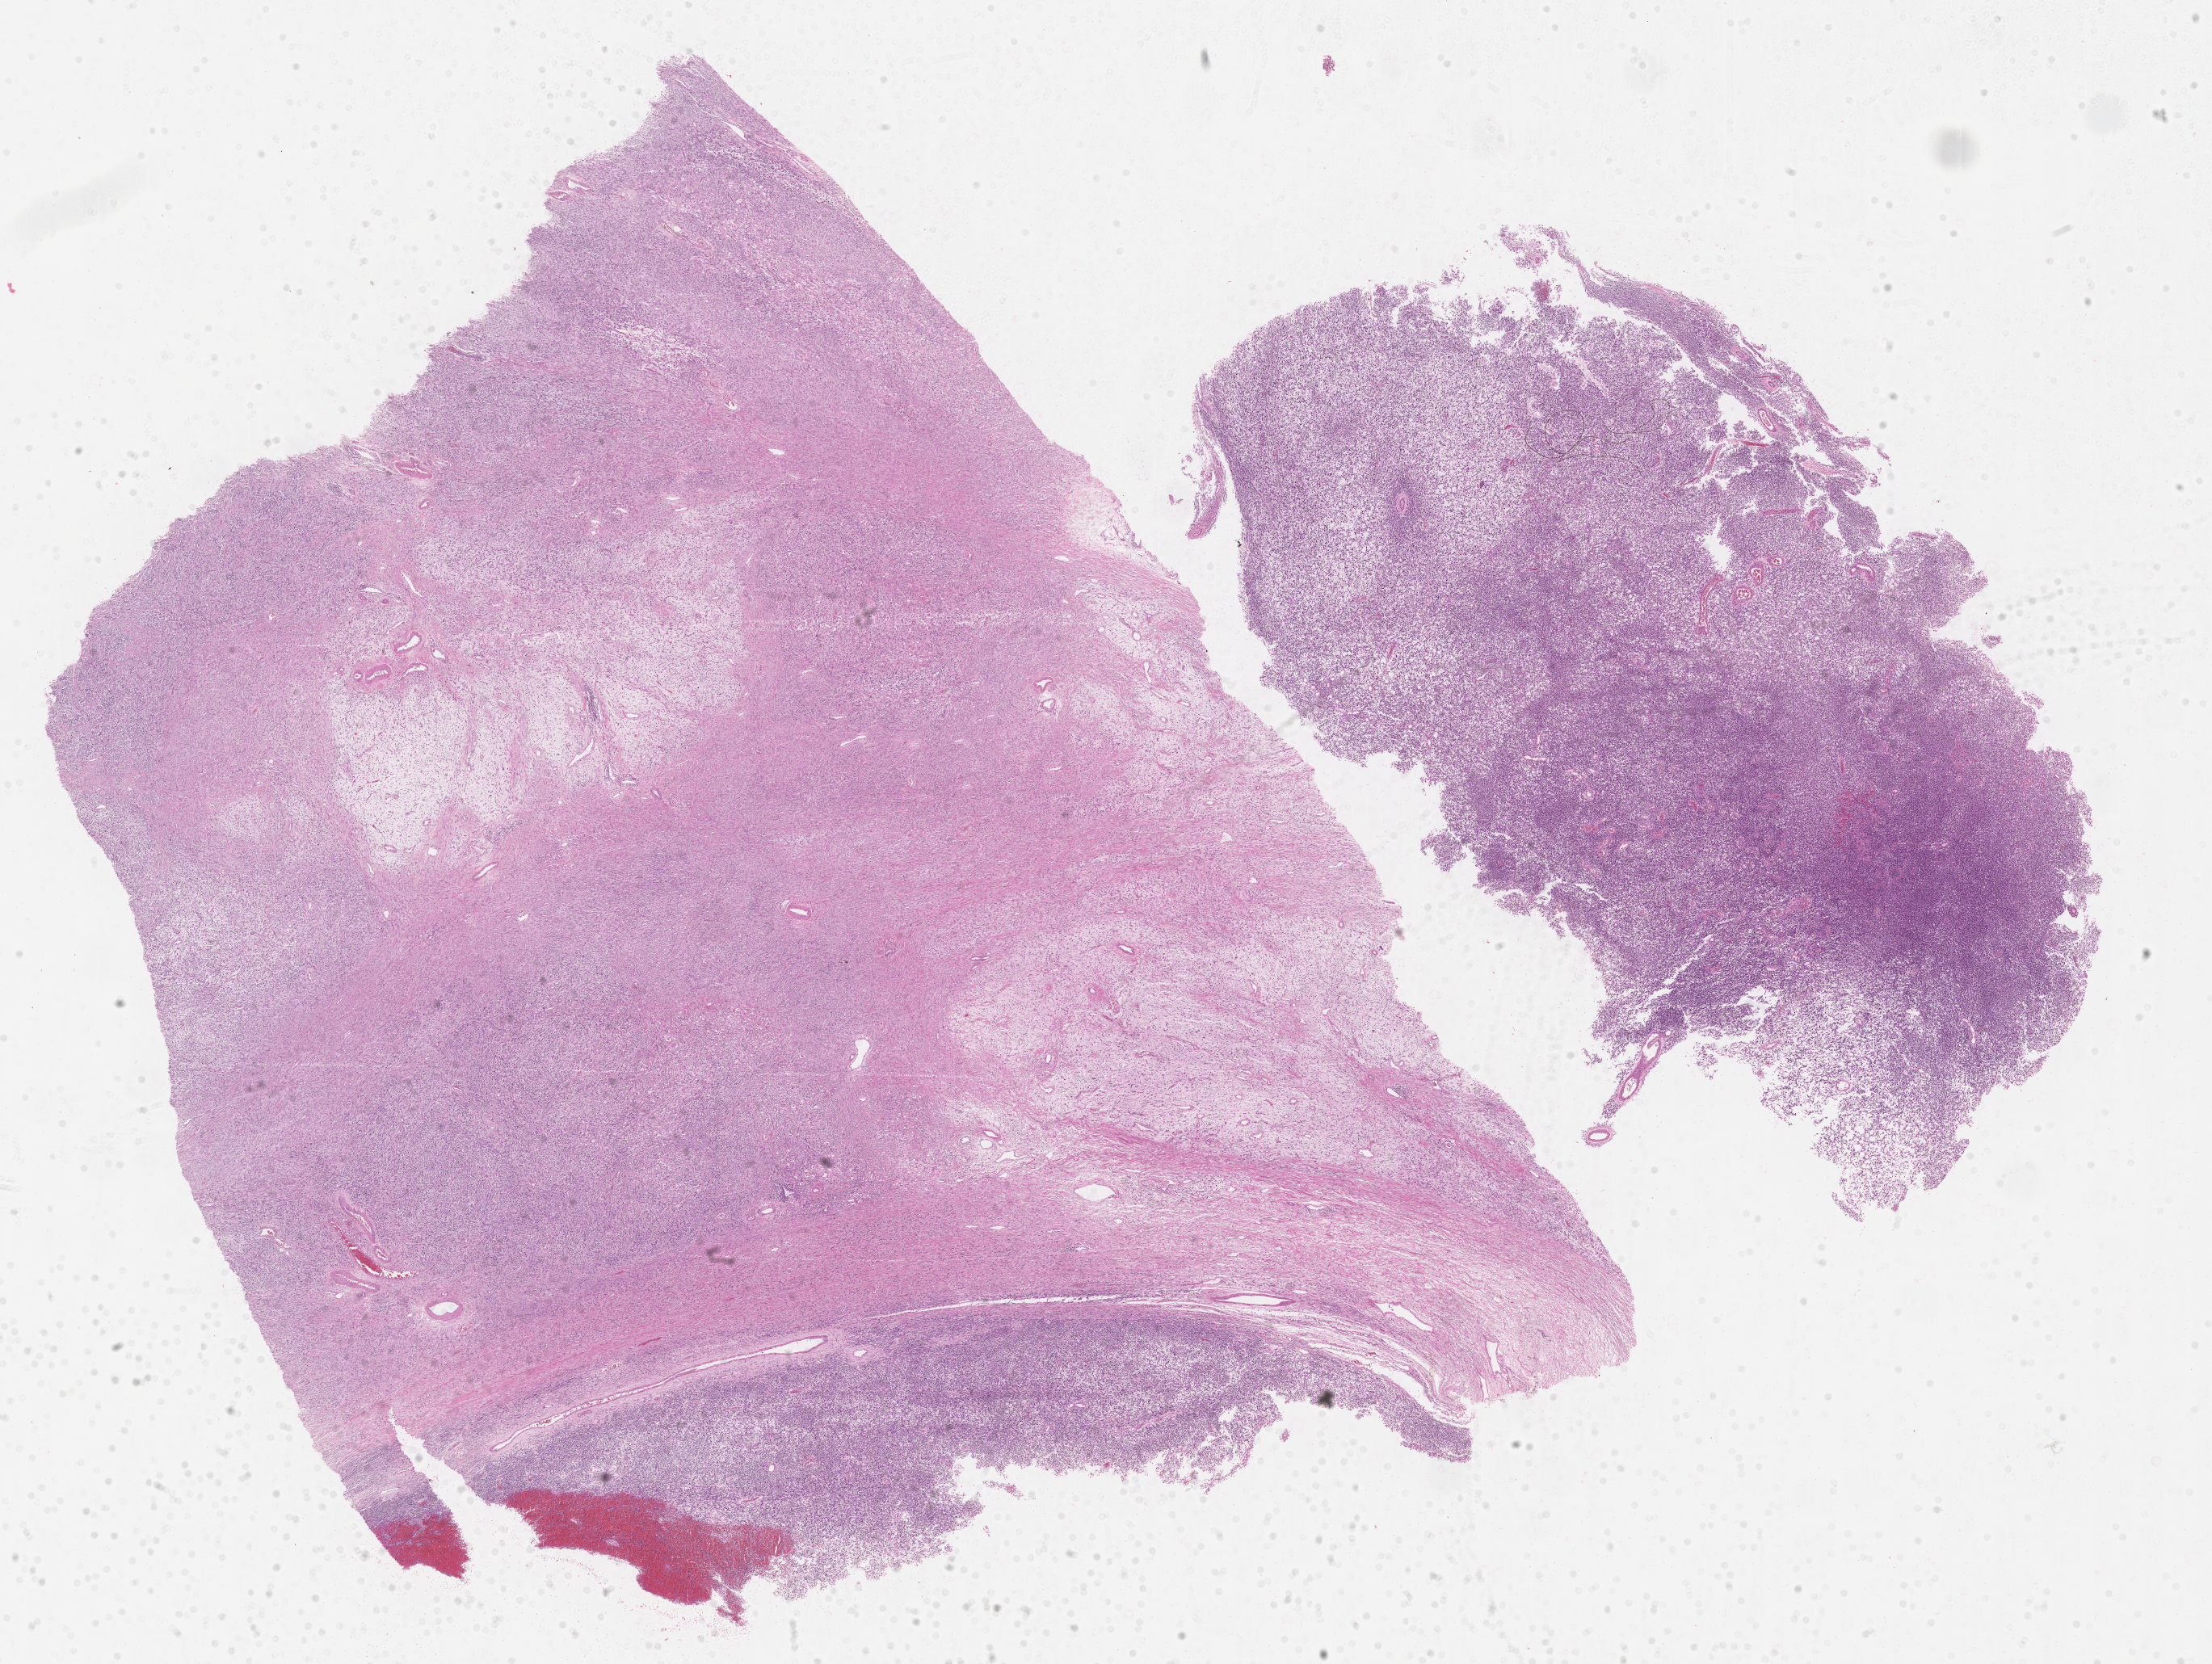
Whole-slide image, haematoxylin and eosin stain of tumor tissue — shown as a low-resolution overview of the whole scanned area (about 22.1 x 16.7 mm), formalin-fixed paraffin-embedded section, site: testicle, right. Patient: male, age 21.3 years at diagnosis.
Diagnosis: rhabdomyosarcoma; histological classification: embryonal rhabdomyosarcoma.